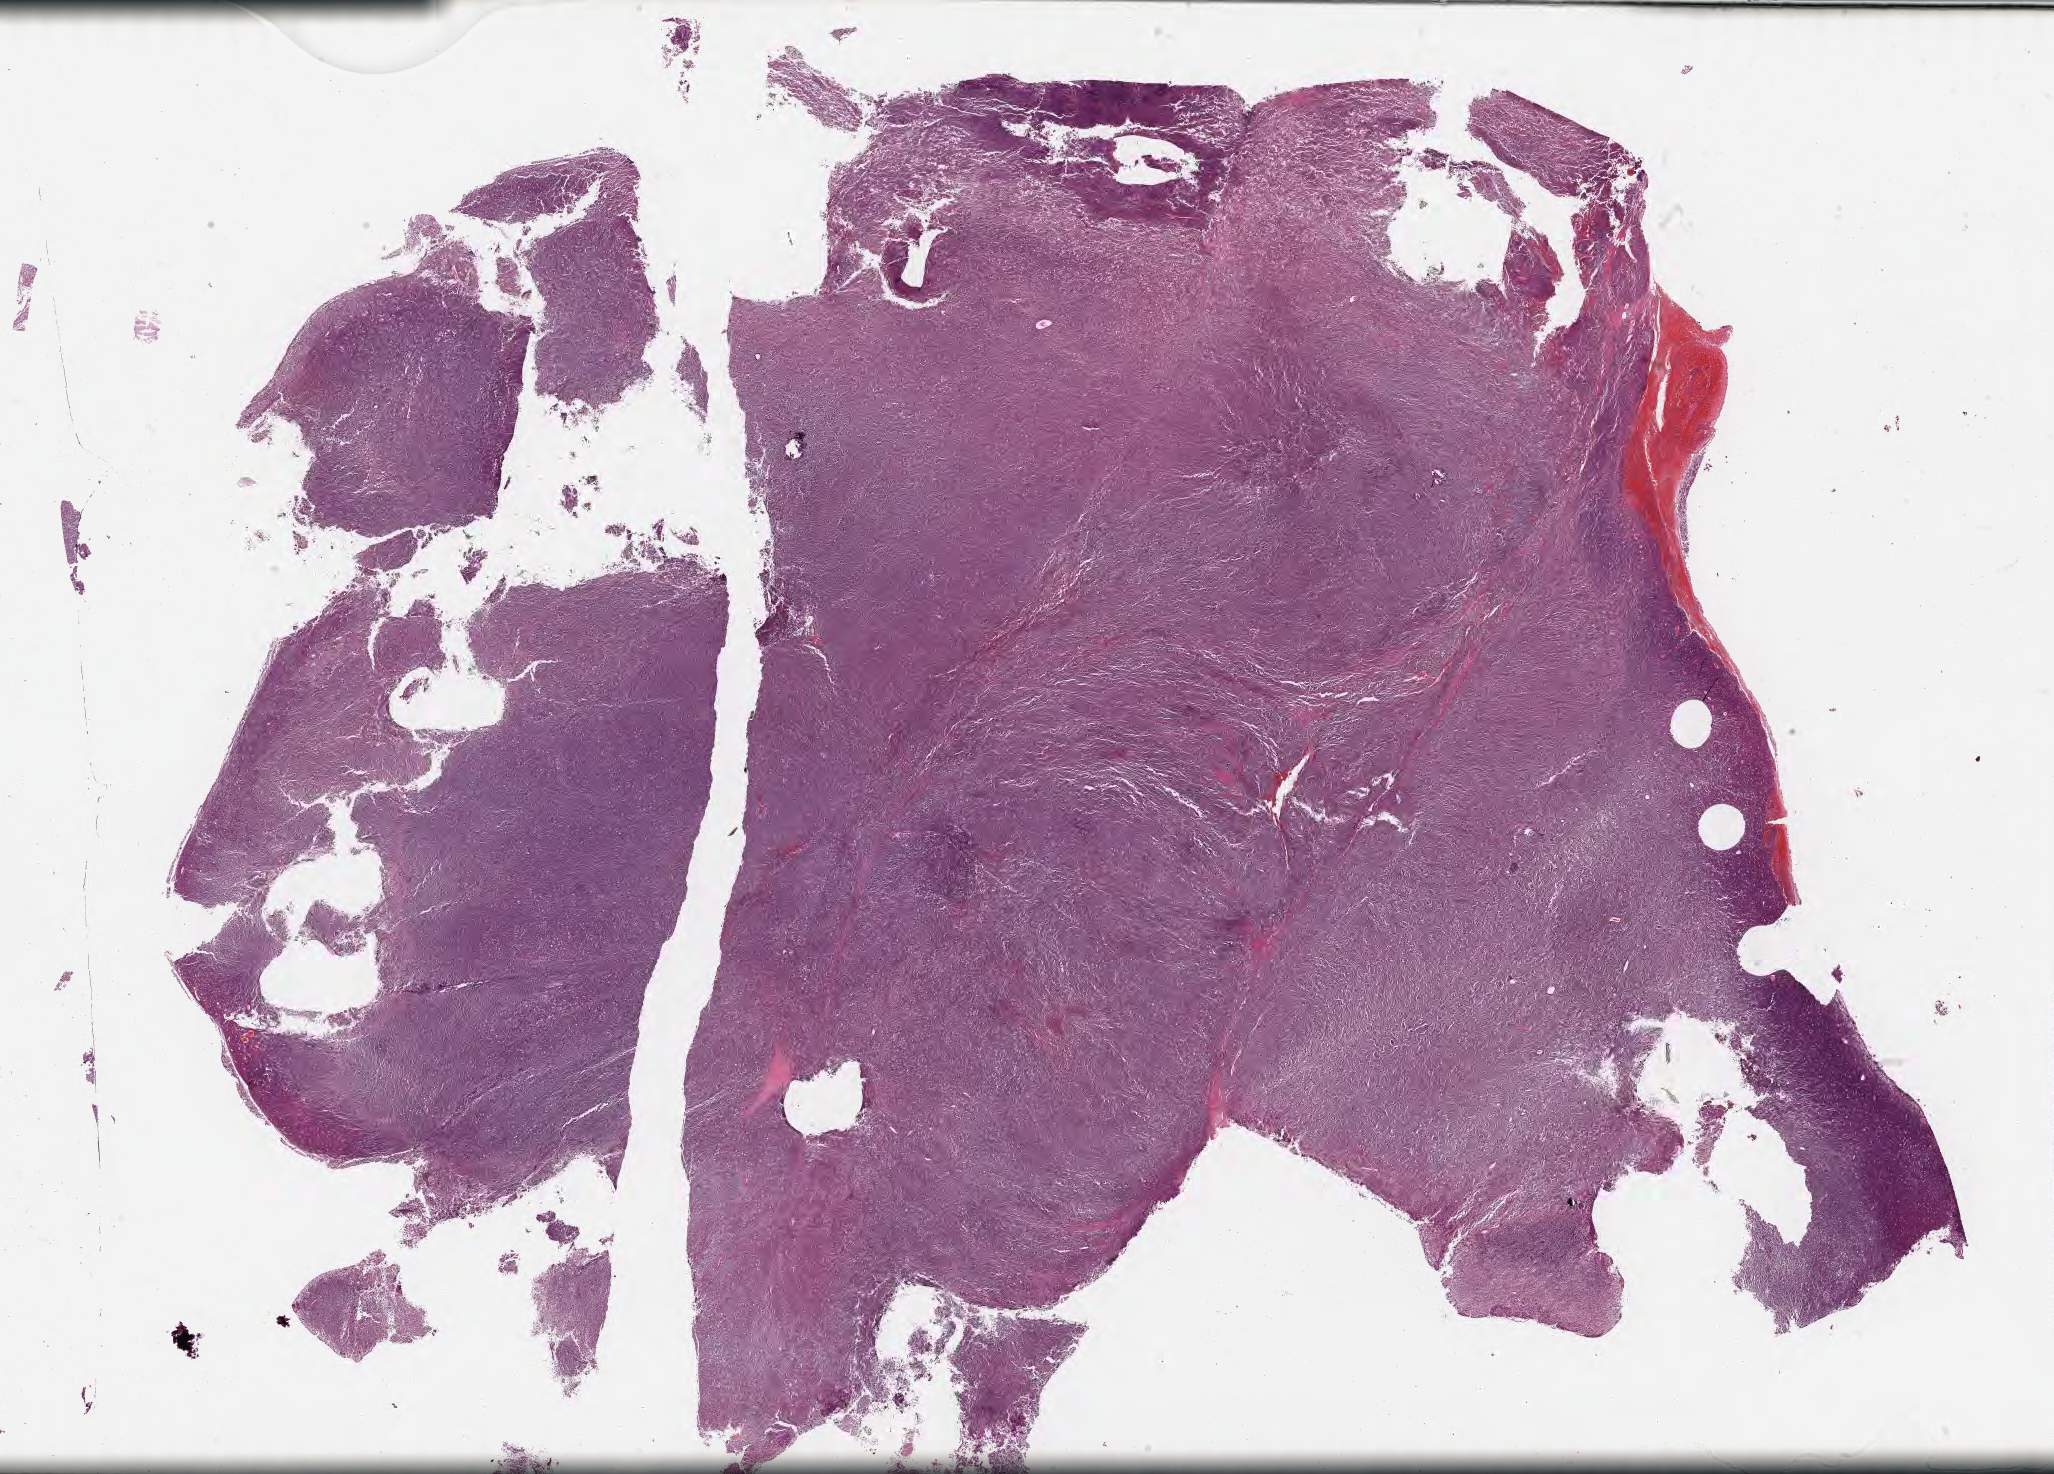
Whole-slide image, H&E stain, low-resolution overview of the scanned area, about 33.2 x 23.8 mm. Formalin-fixed paraffin-embedded section. Primary tumor. Patient: male, 15 years old. Pathologist review of this section (percent, as recorded): tumor cells 90%, tumor nuclei 95%, stromal cells 5%, necrosis 5%, normal cells 0%. Infiltration values recorded for this section: lymphocyte infiltration 40%, monocyte infiltration 35%, neutrophil infiltration 5%.
* histologic diagnosis: Burkitt lymphoma, NOS
* Ann Arbor stage (patient): Stage IV